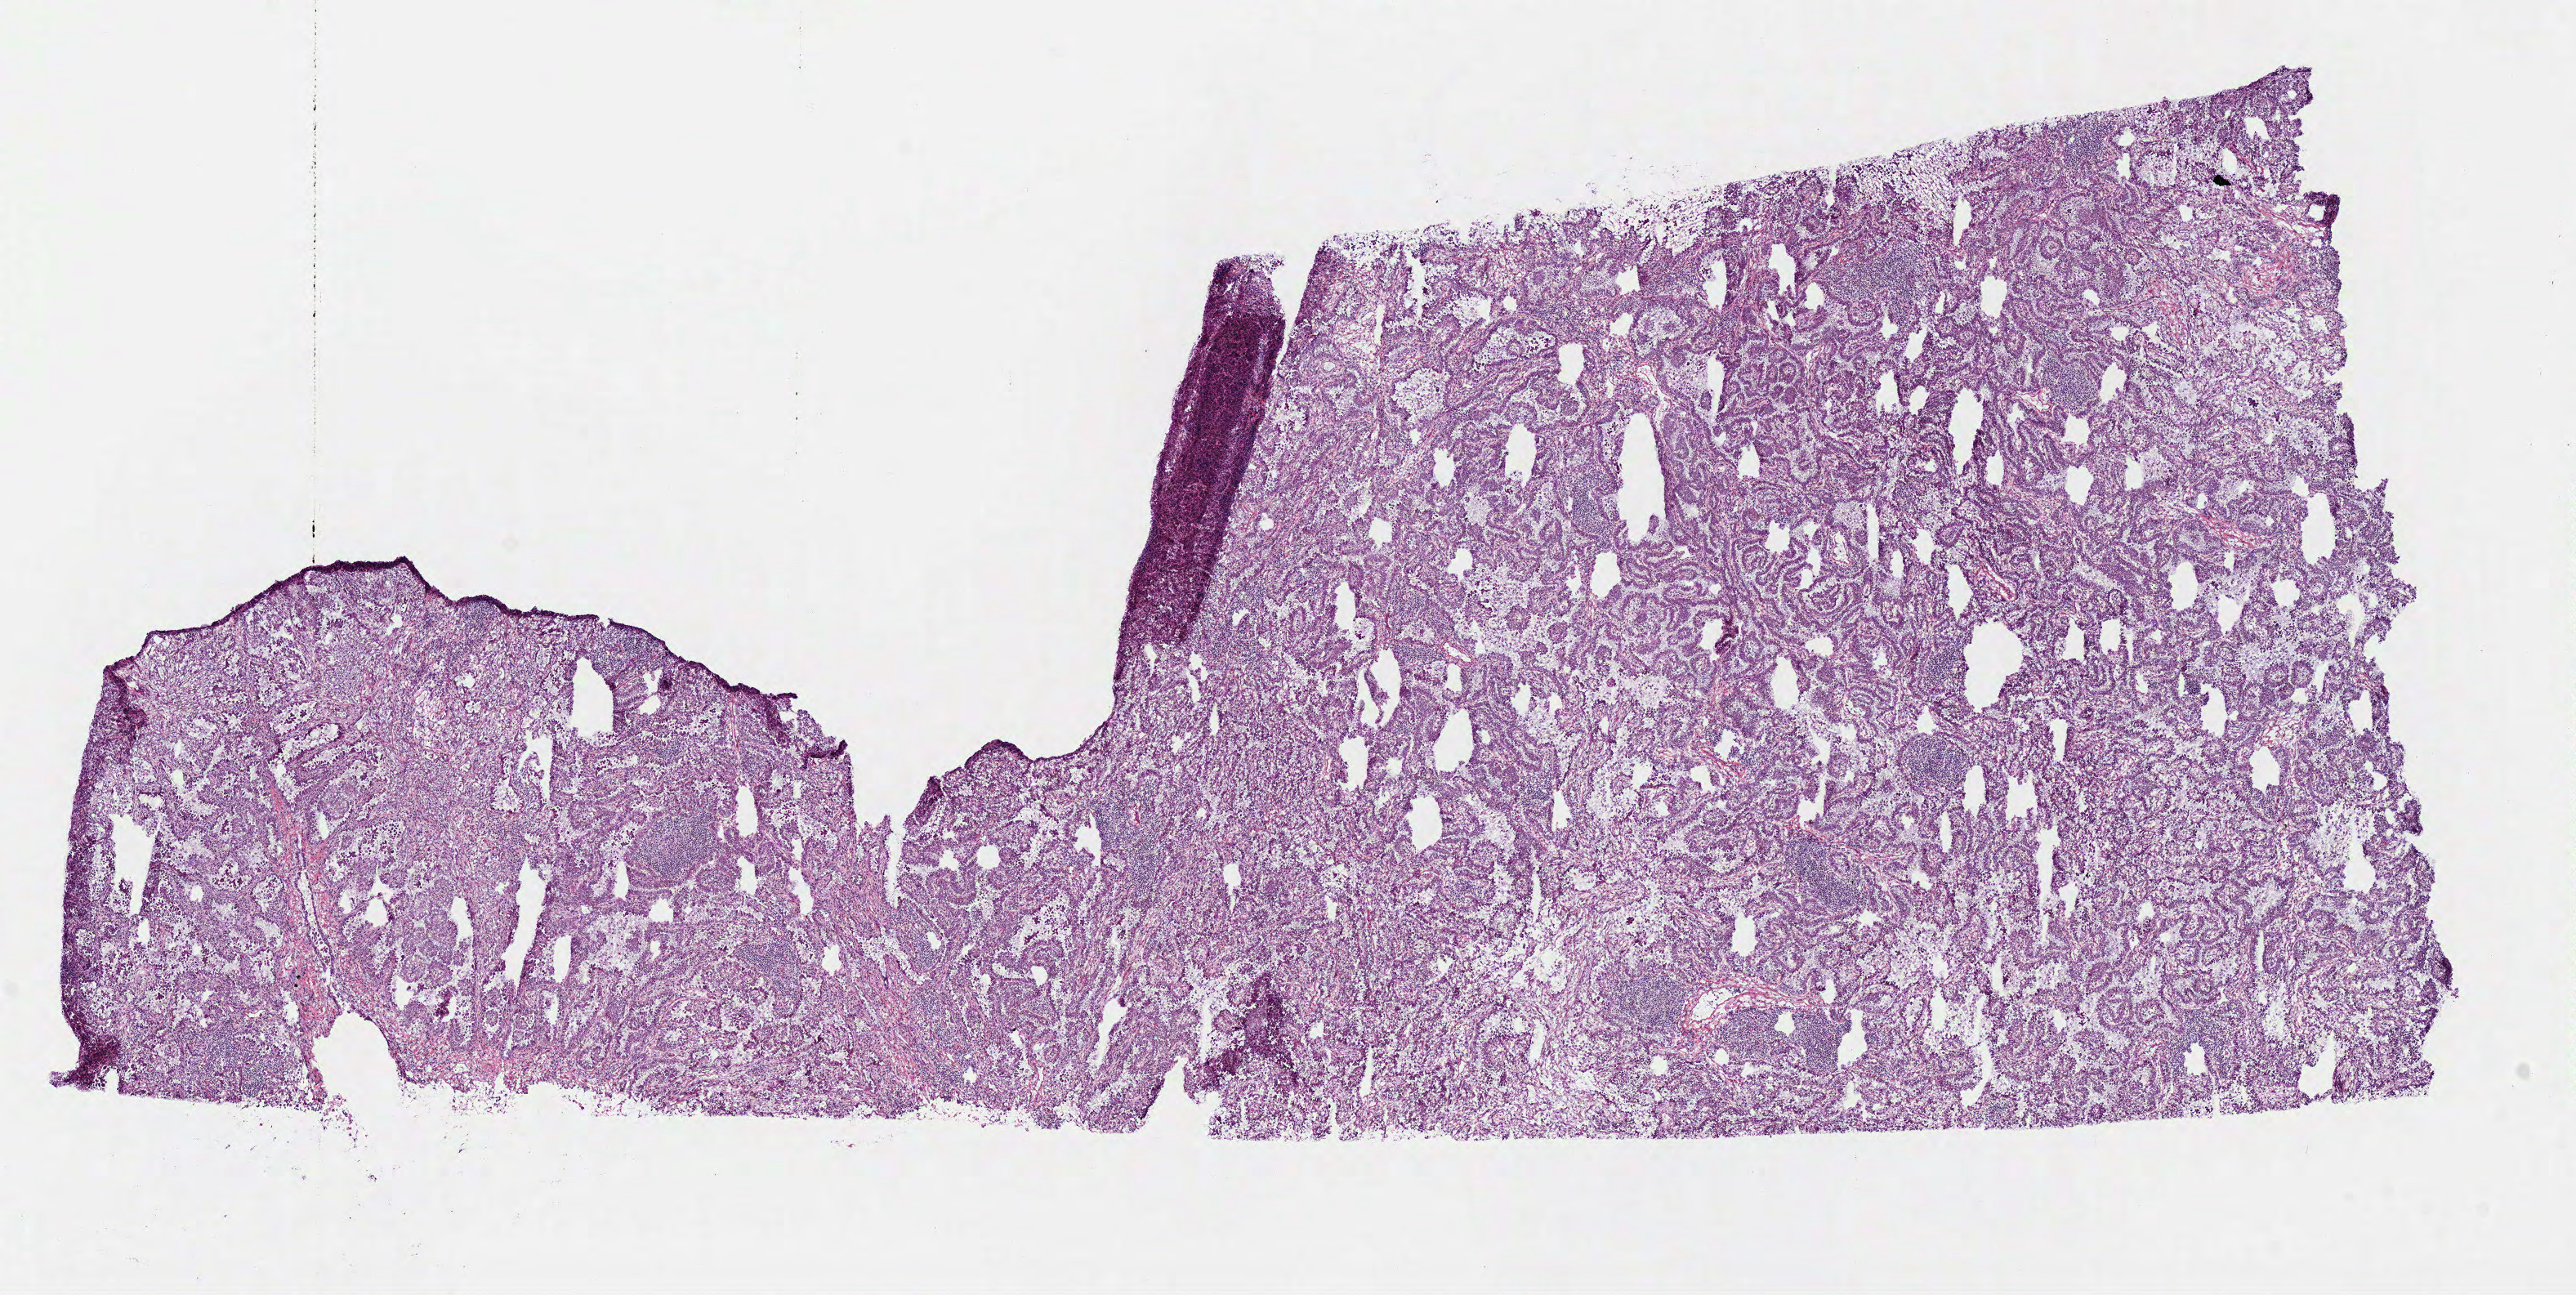
Hematoxylin and eosin (H&E) stained whole-slide image, low-resolution overview of the scanned area, about 12.4 x 6.2 mm (slide scanned at 40x). Frozen section from the top of the tissue portion. Lung, primary tumour sample. Patient sex: female.
Diagnosis: Invasive micropapillary carcinoma (lower lobe, lung).